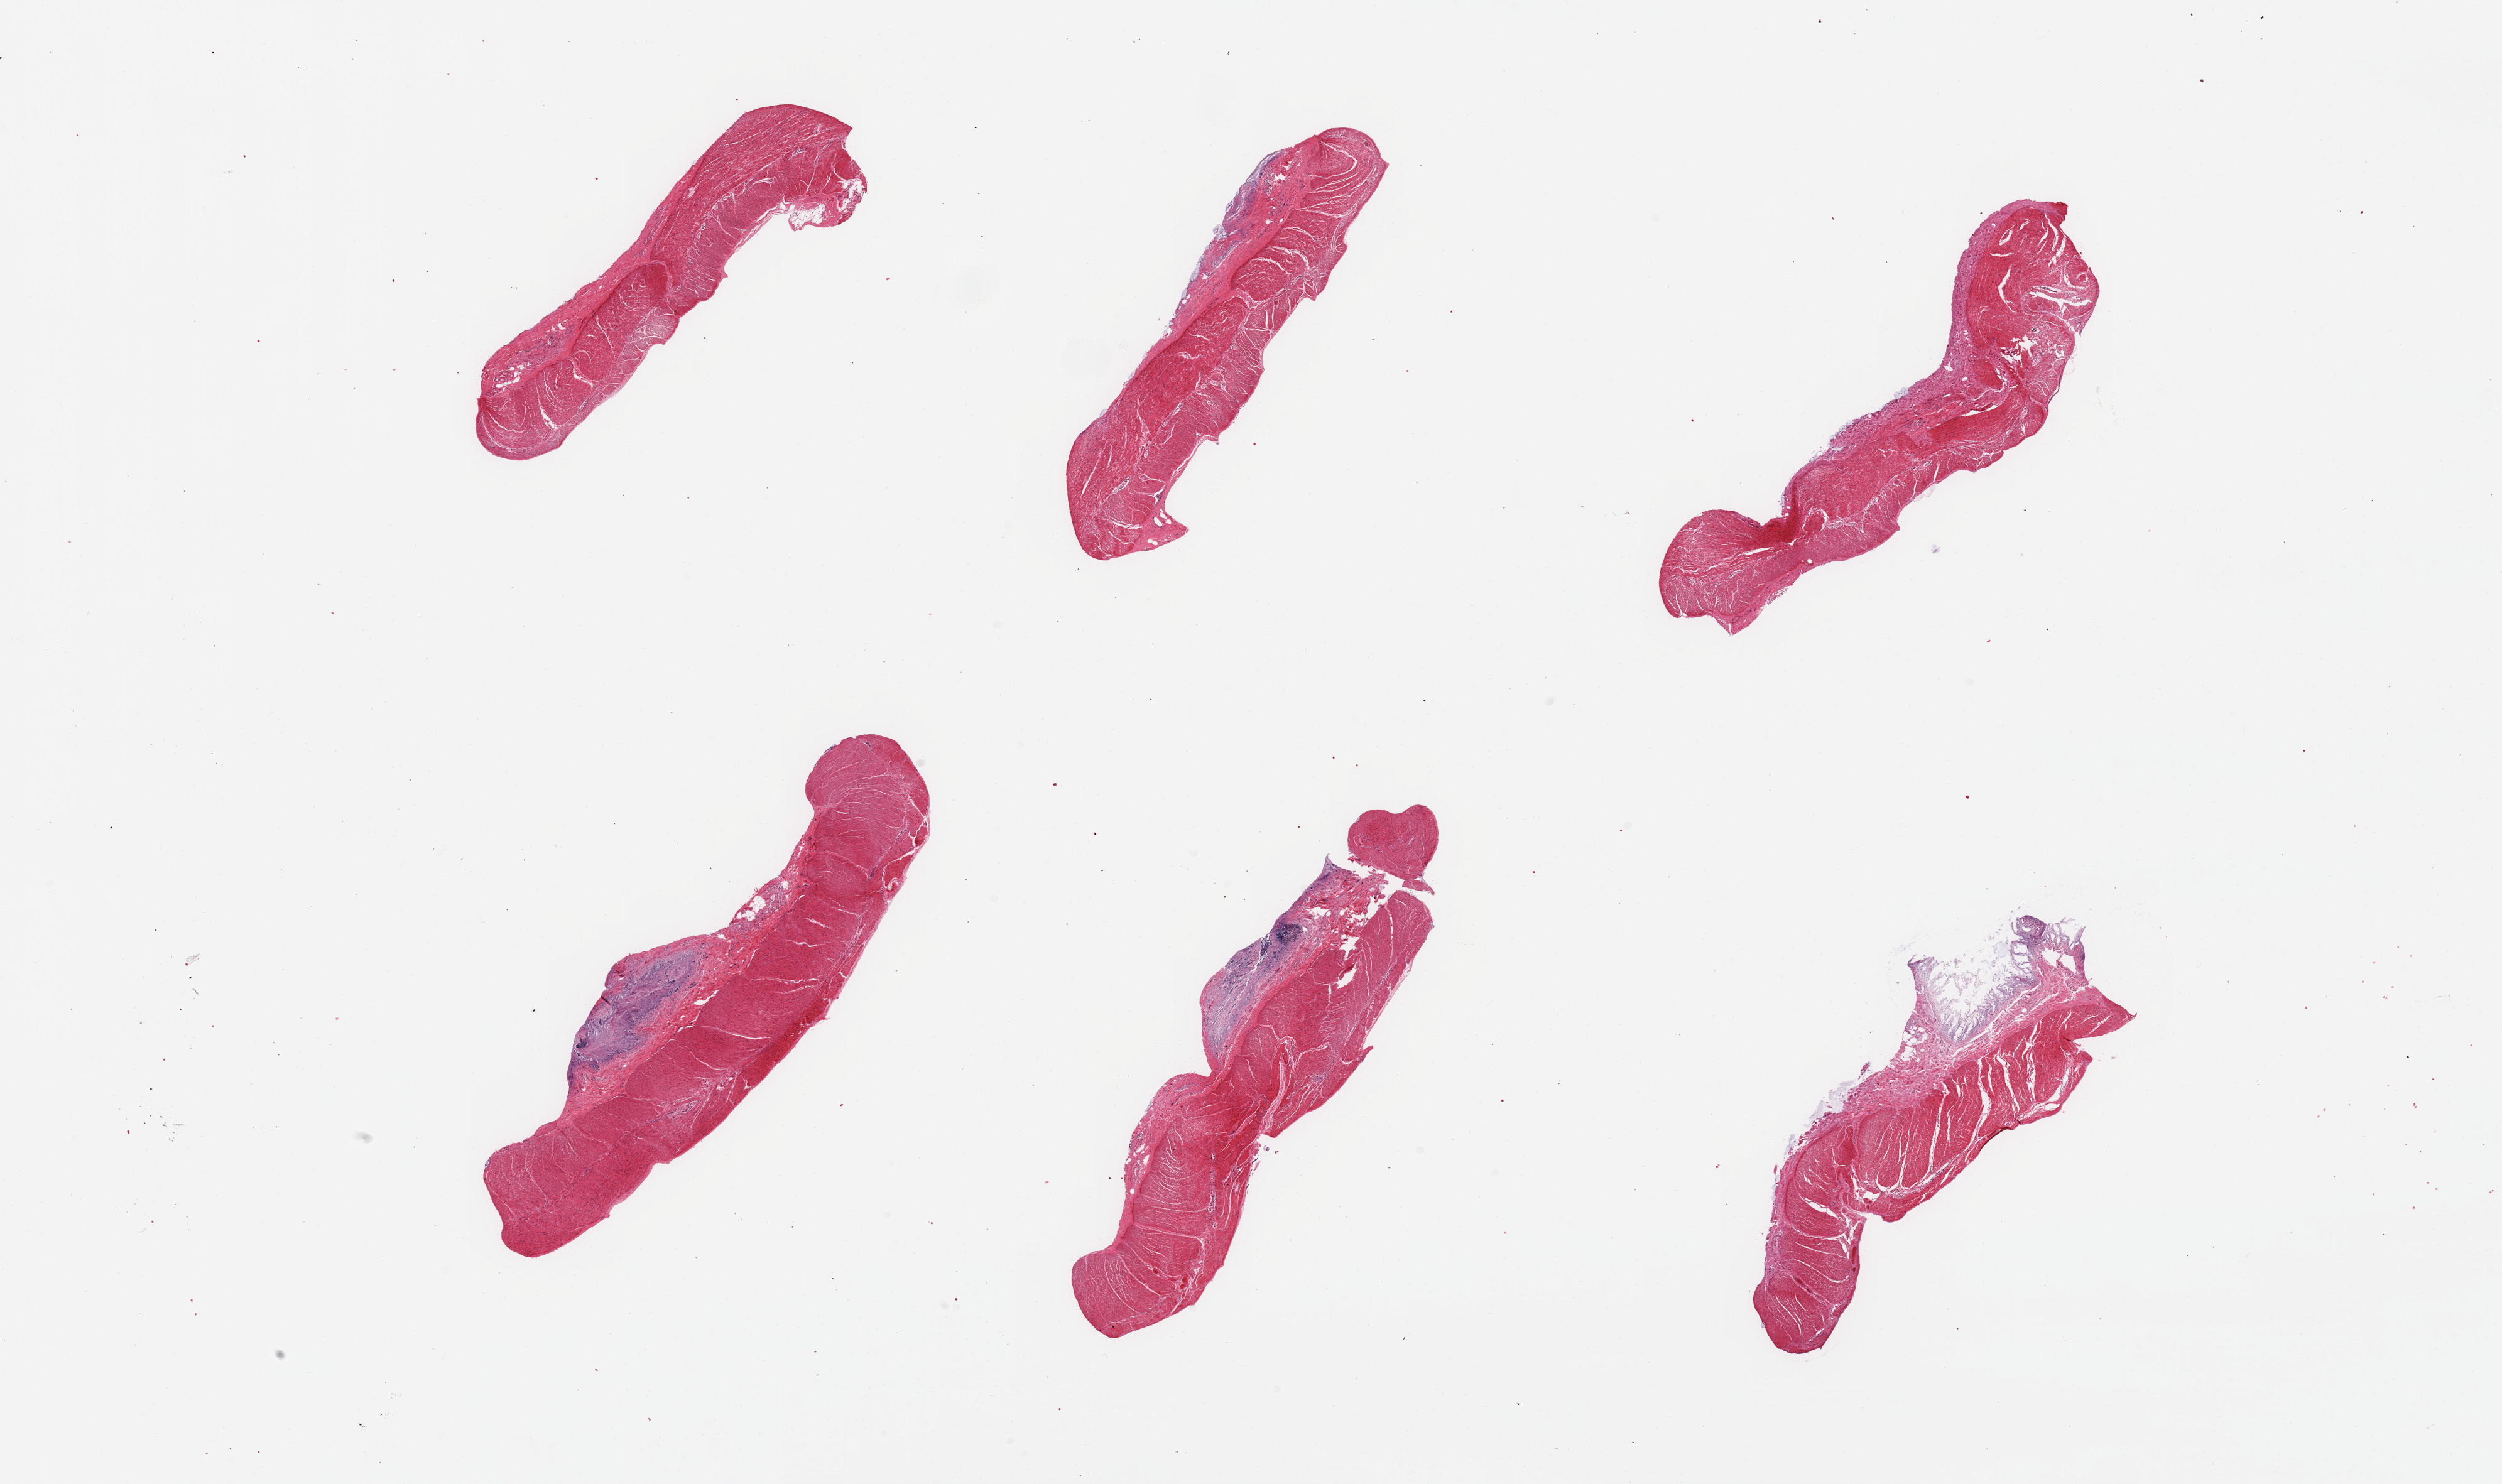
Digitized hematoxylin and eosin (H&E)-stained section, brightfield, shown as a low-resolution overview of the whole scanned area (about 31.5 x 18.7 mm), PAXgene-fixed, paraffin-embedded tissue, section of transverse colon (target tissue), donor tissue sample. Donor: female.
Review note (as recorded): 6 pieces; predominantly muscularis, few residual strips of autolyzed mucosa.